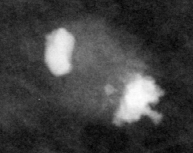
Region of interest cut from a scanned film mammogram (one marked finding), left breast, MLO view, BI-RADS breast density category 1 (scale 1–4).
Calcifications, morphology coarse; BI-RADS assessment category 2; benign without callback (not worked up further).